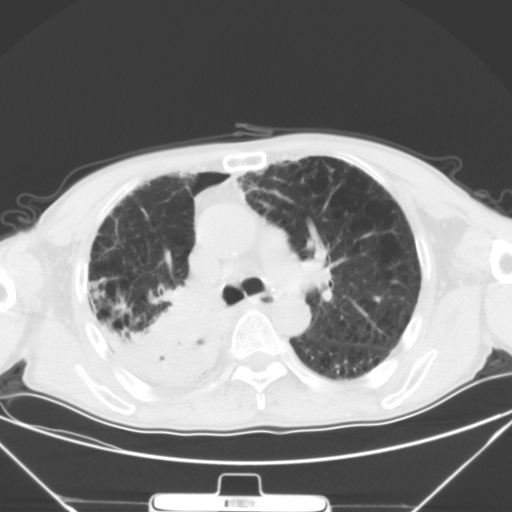
Chest CT, one axial slice. Slice 31 of 50 in the series (ordered by position). 120 kVp. Lung window (W 1500 / L -600 HU). 5 mm slice thickness. 512 × 512 image matrix, field of view 373 × 373 mm. Patient: male, 65 years. Case-level facts recorded for this patient, not image findings: clinical TNM (as recorded): T3 N1 M1a.
Annotated regions visible in this slice (rectangle marked by the reading radiologist):
- lung tumour (recorded histology: squamous cell carcinoma): box from (x=139, y=280) to (x=222, y=389) px